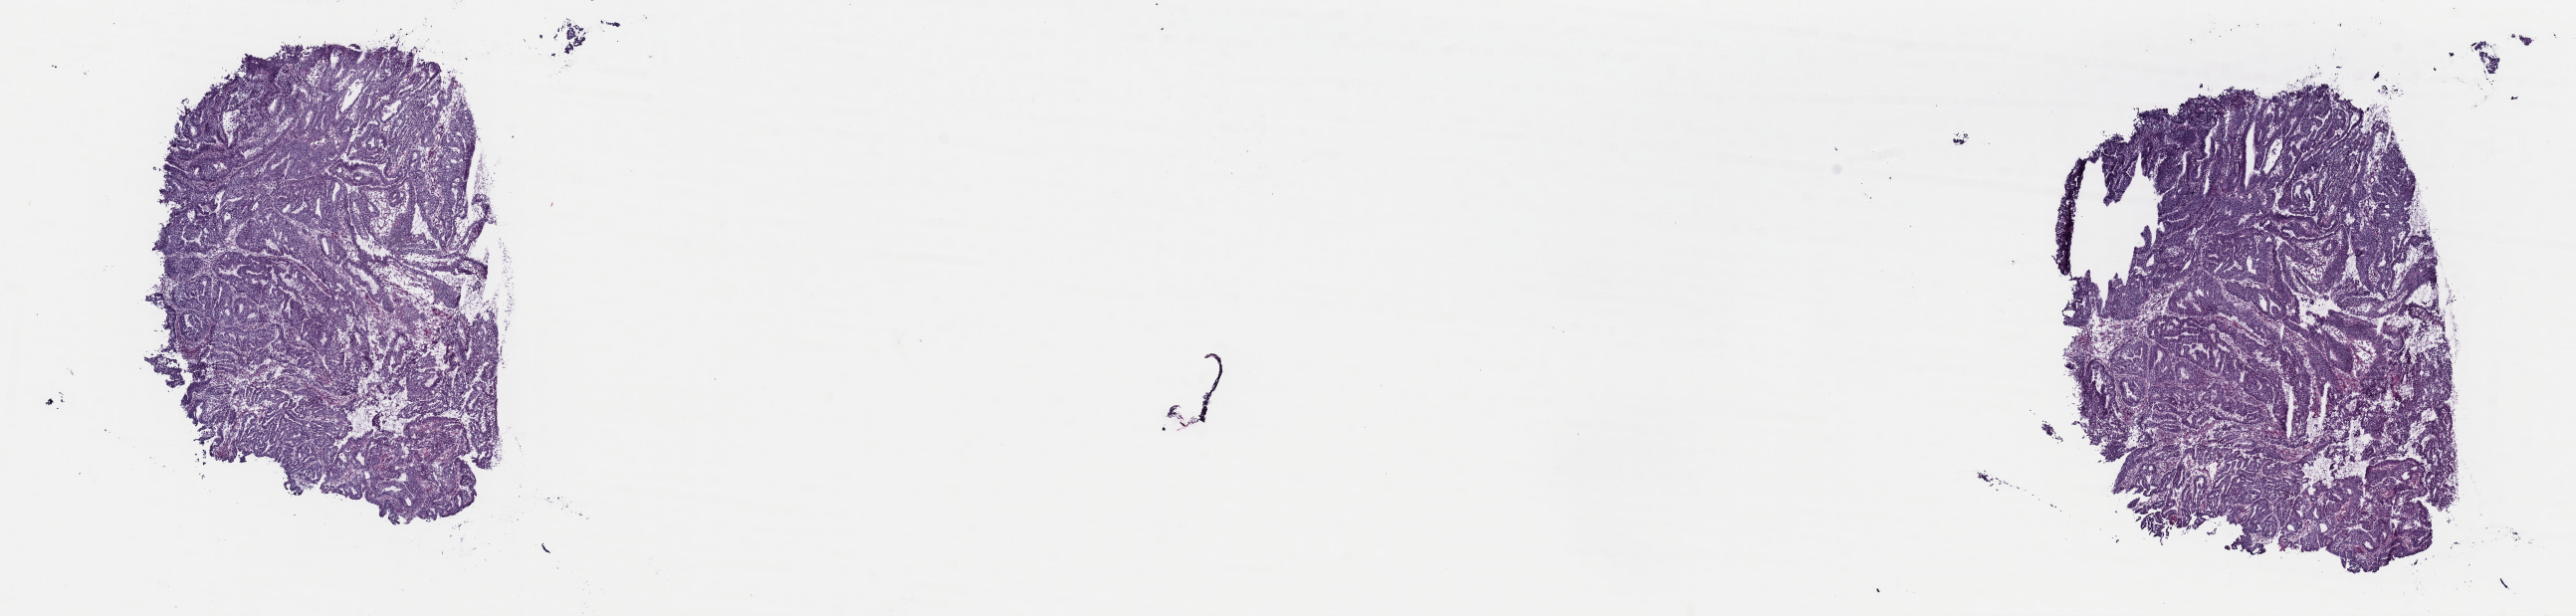
Whole-slide histology image, H&E — low-resolution overview of the scanned area, about 20.4 x 4.9 mm, frozen section from the top of the tissue portion, uterus, primary tumour sample. Patient: female, age at initial diagnosis 56 years. Histologic grade: G2 (moderately differentiated). Slide review estimates, as recorded: tumour cells 100%, tumour nuclei 80%, normal cells 0%, stromal cells 0%, necrosis 0%. Infiltration values recorded for this section: lymphocyte infiltration 2%, monocyte infiltration 0%, neutrophil infiltration 0%.
FIGO stage: IA. Lymph nodes positive (case pathology): 0 of 13 examined. Histologic diagnosis: Endometrioid adenocarcinoma, NOS (endometrium).